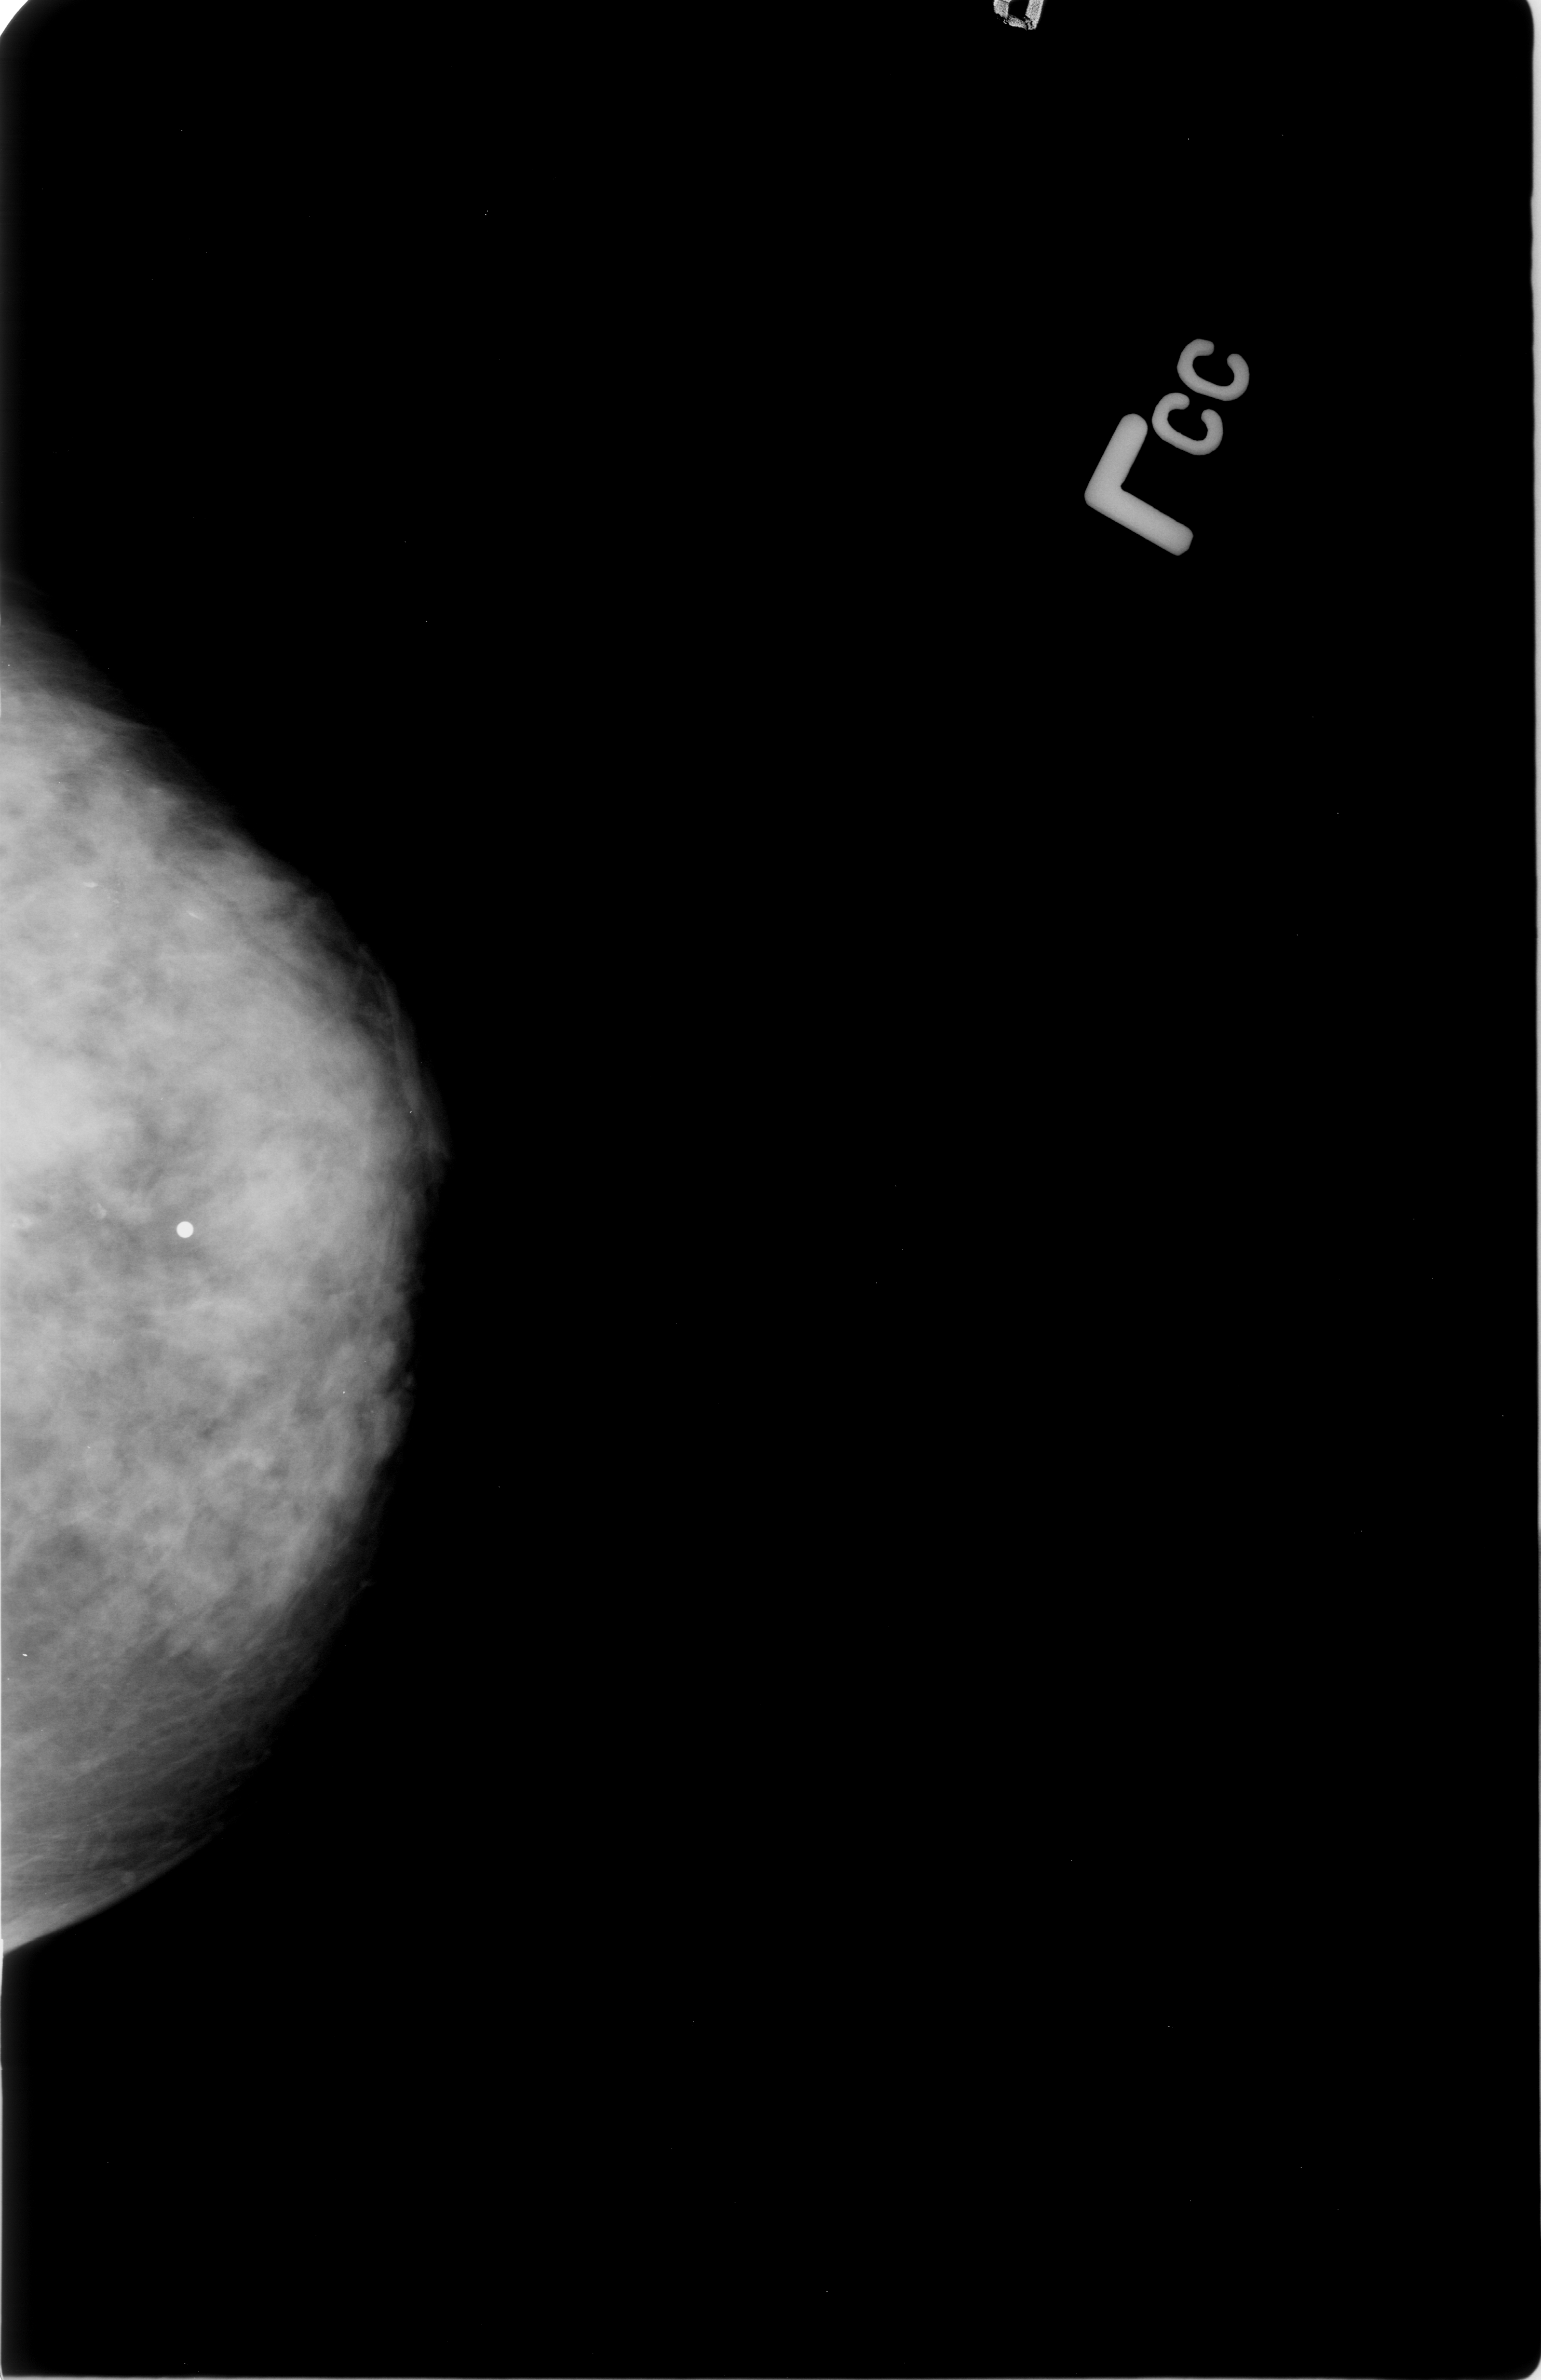
Scanned film-screen mammogram; left breast; CC view.
Calcifications, morphology pleomorphic, distribution clustered; BI-RADS assessment category 4; pathology (as recorded): malignant.